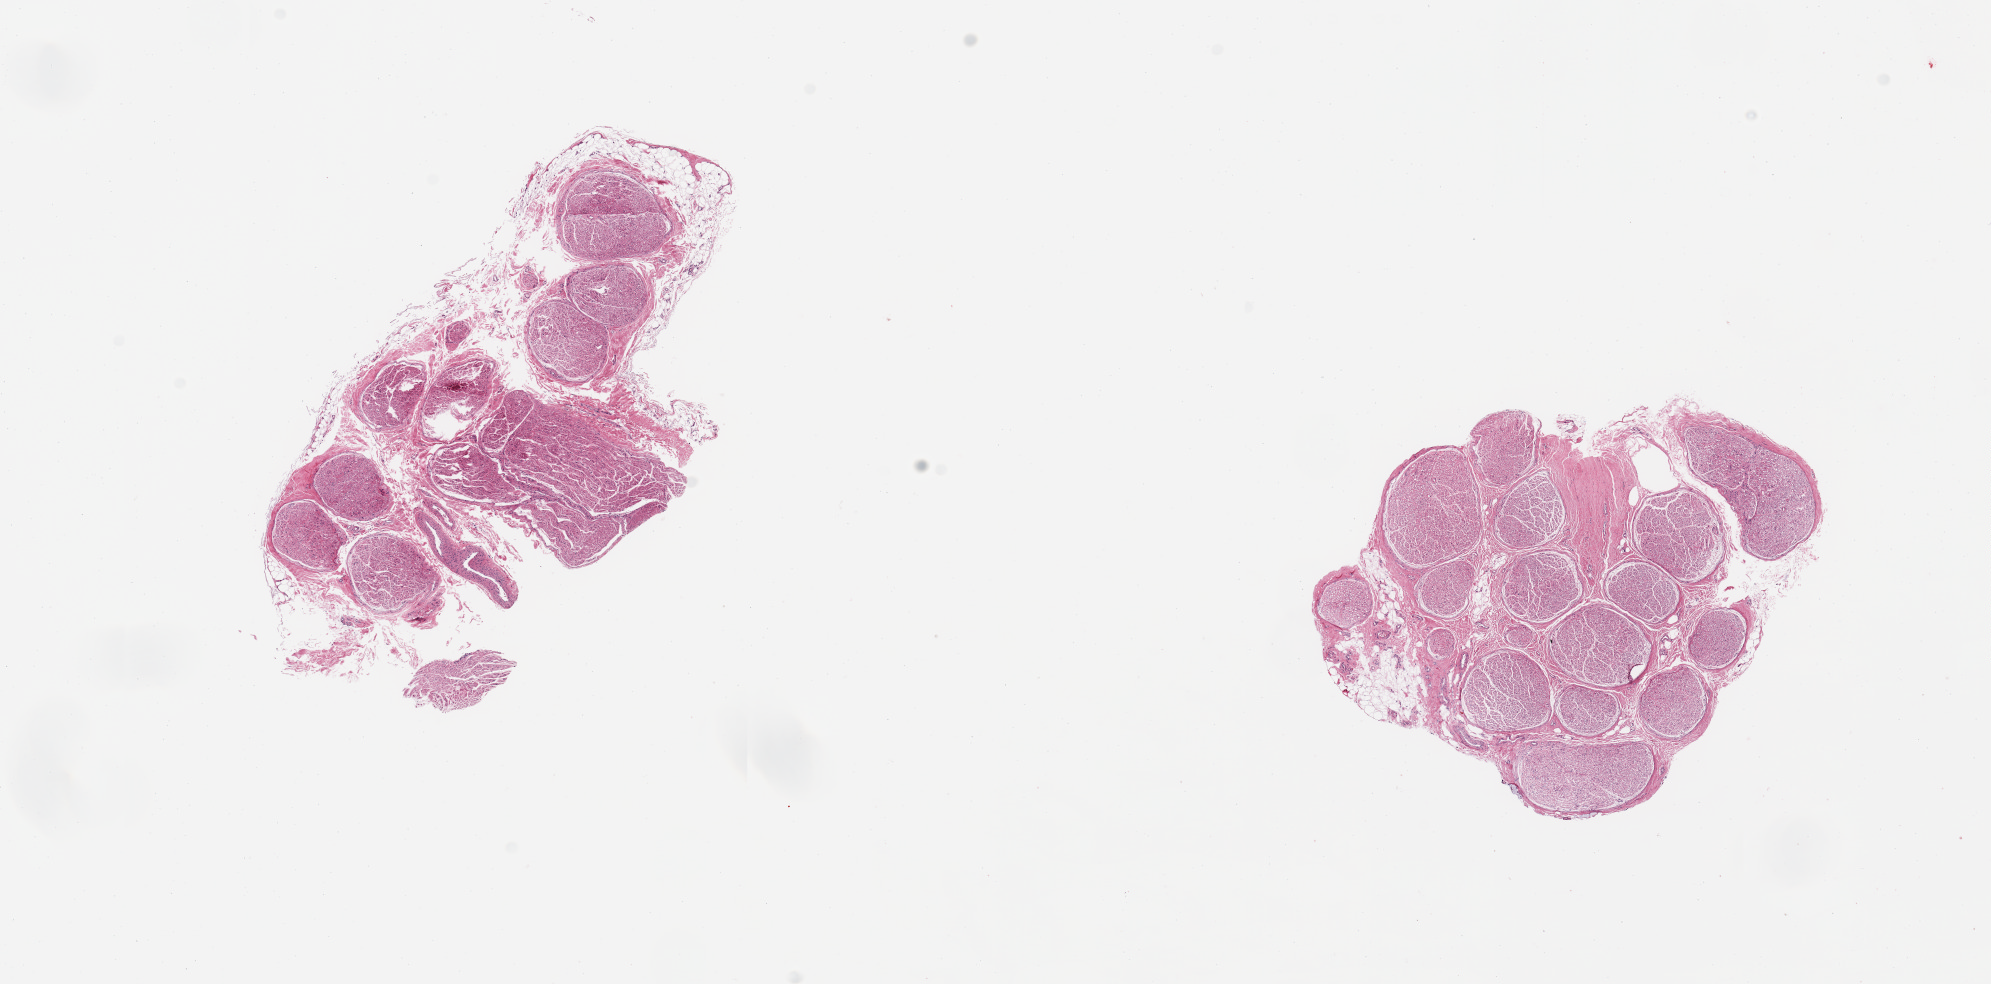
Whole-slide image, hematoxylin and eosin (H&E) stain — a low-resolution overview of the entire scanned area, about 15.8 x 7.8 mm (slide scanned at 20x), PAXgene-fixed, paraffin-embedded tissue, sampled site (target tissue): tibial nerve, tissue donor sample.
• pathologist's review note for this sample: 2 pieces; 10% & 30% fat content